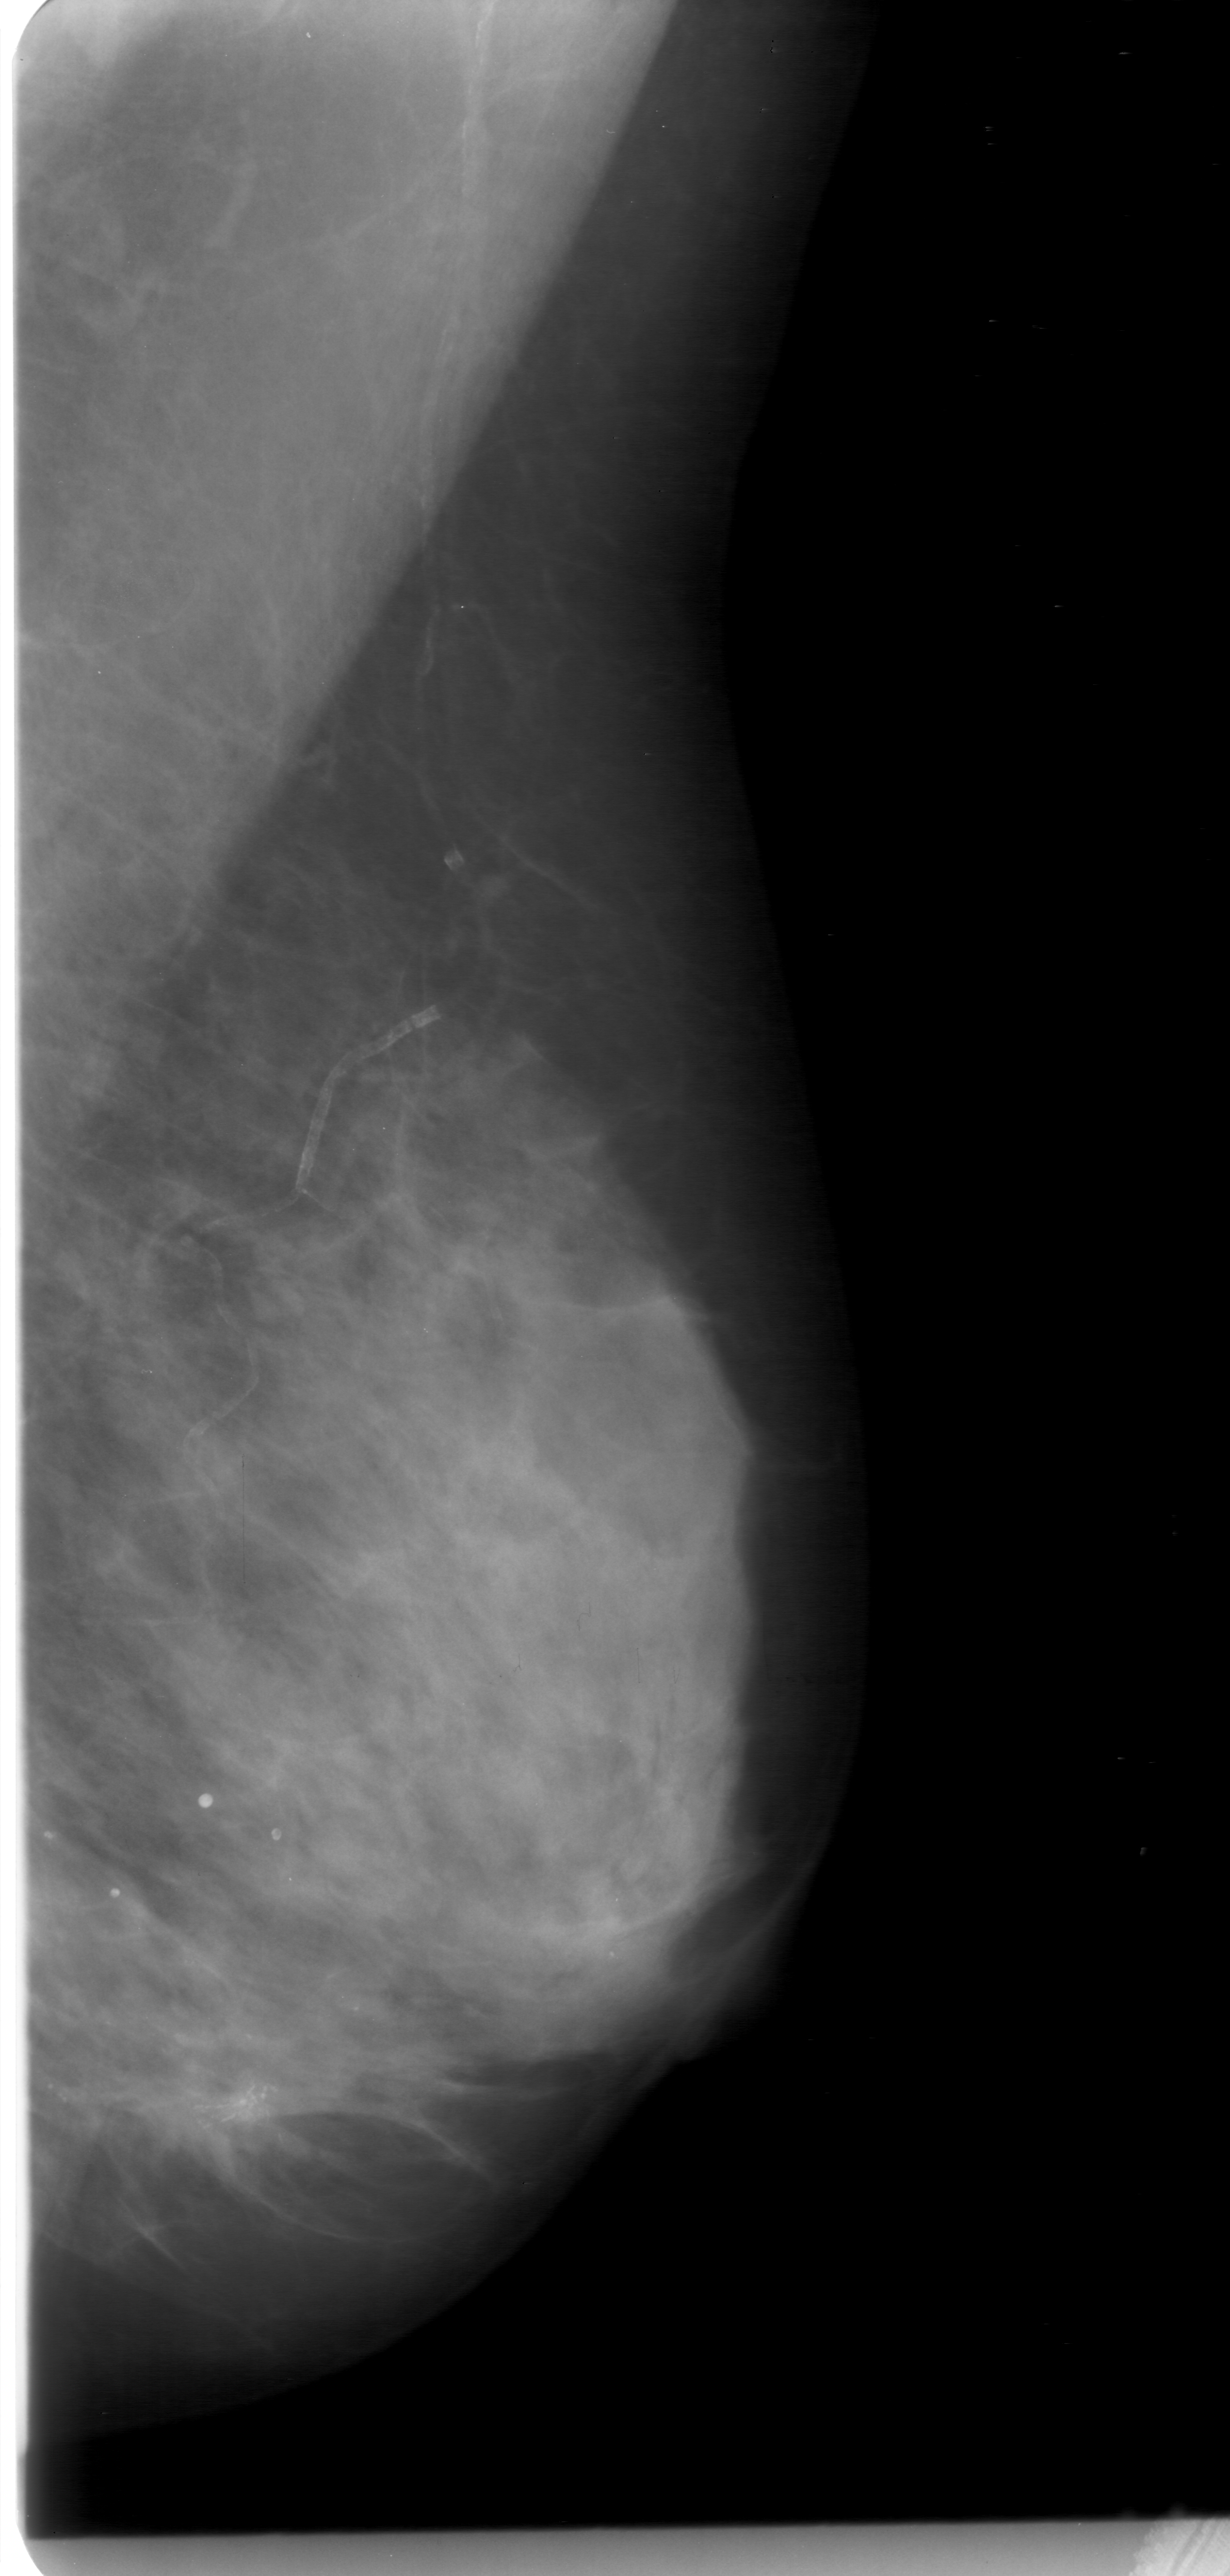
Scanned film-screen mammogram, left breast, MLO view, BI-RADS breast density category 3 (scale 1–4).
- Abnormality record for this image: calcifications, morphology fine linear branching, distribution clustered; BI-RADS assessment category 5; pathology (as recorded): malignant.